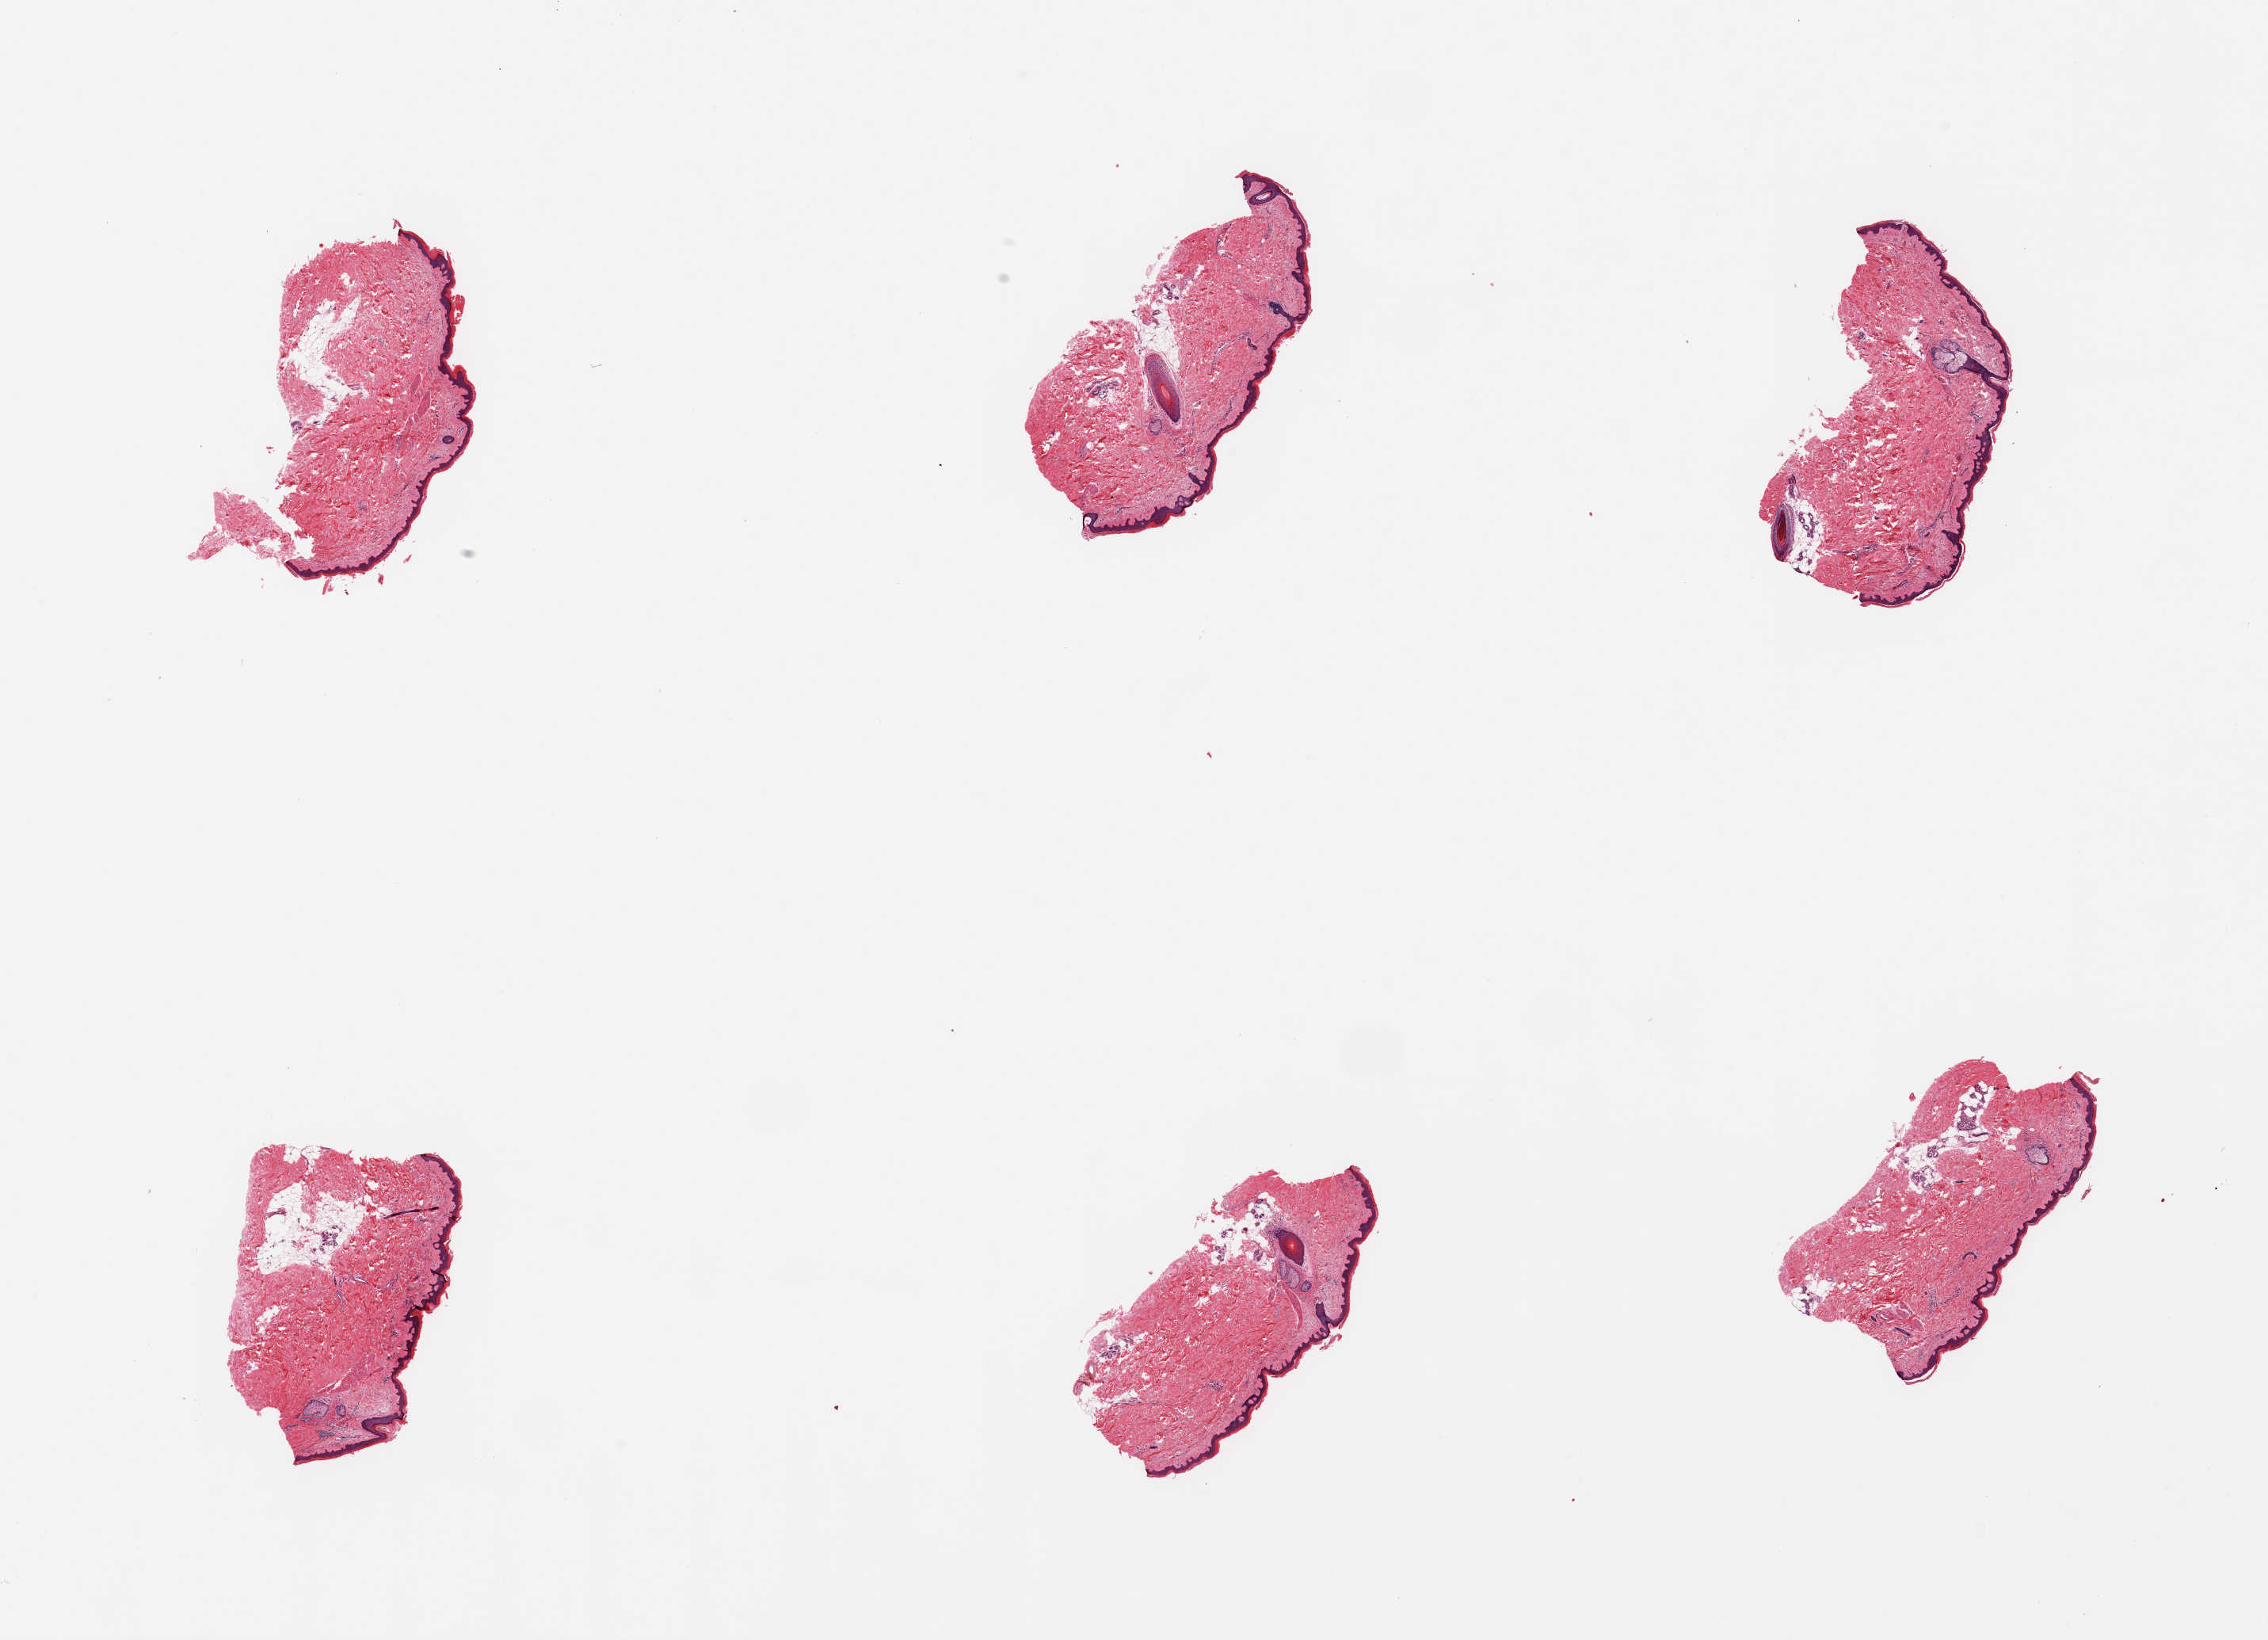
H&E whole-slide image, whole scanned area (about 22.6 x 16.4 mm) shown as a low-resolution overview. PAXgene-fixed paraffin-embedded (PFPE) section. Sampled site (target tissue): skin of lower leg. Donor tissue sample. Male donor.
* pathologist's review note for this sample: 6 pieces; include from 5-10% internal fat, epidermis measures about 34 microns